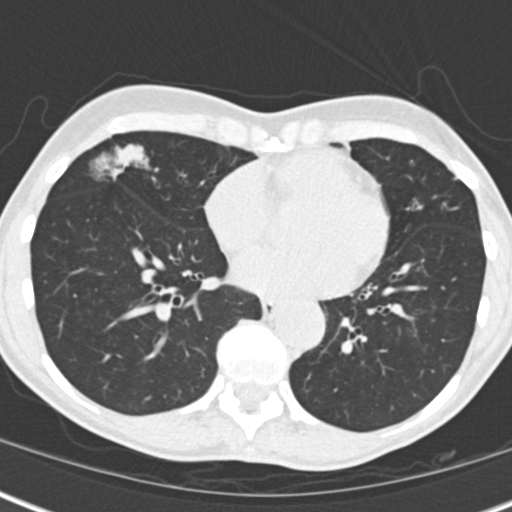
Low-dose screening chest CT, one axial slice. Slice 68 of 173 in the series (ordered by position). Lung window (W 1500 / L -600 HU). 512 × 512 image matrix.
Structures marked on this image (manually delineated by an expert):
- lesion 1 (tumor, middle lobe of right lung): bounding box (x1, y1, x2, y2) in pixels: (115, 145, 147, 166)